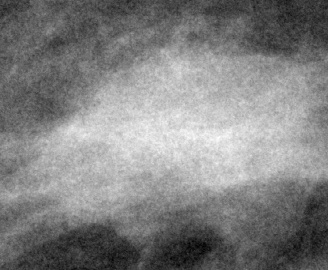
Region of interest cut from a scanned film mammogram (one marked finding); right breast; CC view; BI-RADS breast density category 2 (scale 1–4).
Mass, shape irregular, margins spiculated; BI-RADS assessment category 4; pathology result (as recorded, not read from the image): malignant.